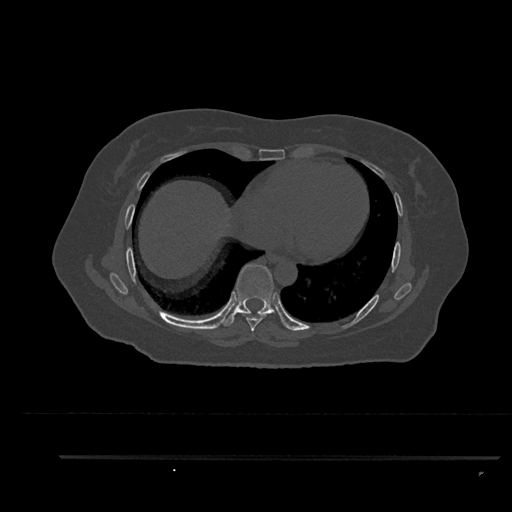
CT including the spine, one axial slice. Position 482 of 797 along the scan axis. Reconstruction kernel Br40s/3. 120 kVp. Bone window (W 1800 / L 400 HU). 512 × 512 image matrix. Female patient, age 44 years. Case-level facts recorded for this patient, not image findings: primary cancer: renal; vertebrae with lytic lesions (as recorded): L1.
Outlined on this slice (semi-automatic segmentation, software-assisted and operator-edited):
- T7 vertebra: bounding box (x1, y1, x2, y2) in pixels: (241, 312, 267, 332)
- T8 vertebra: (223, 264, 286, 327)